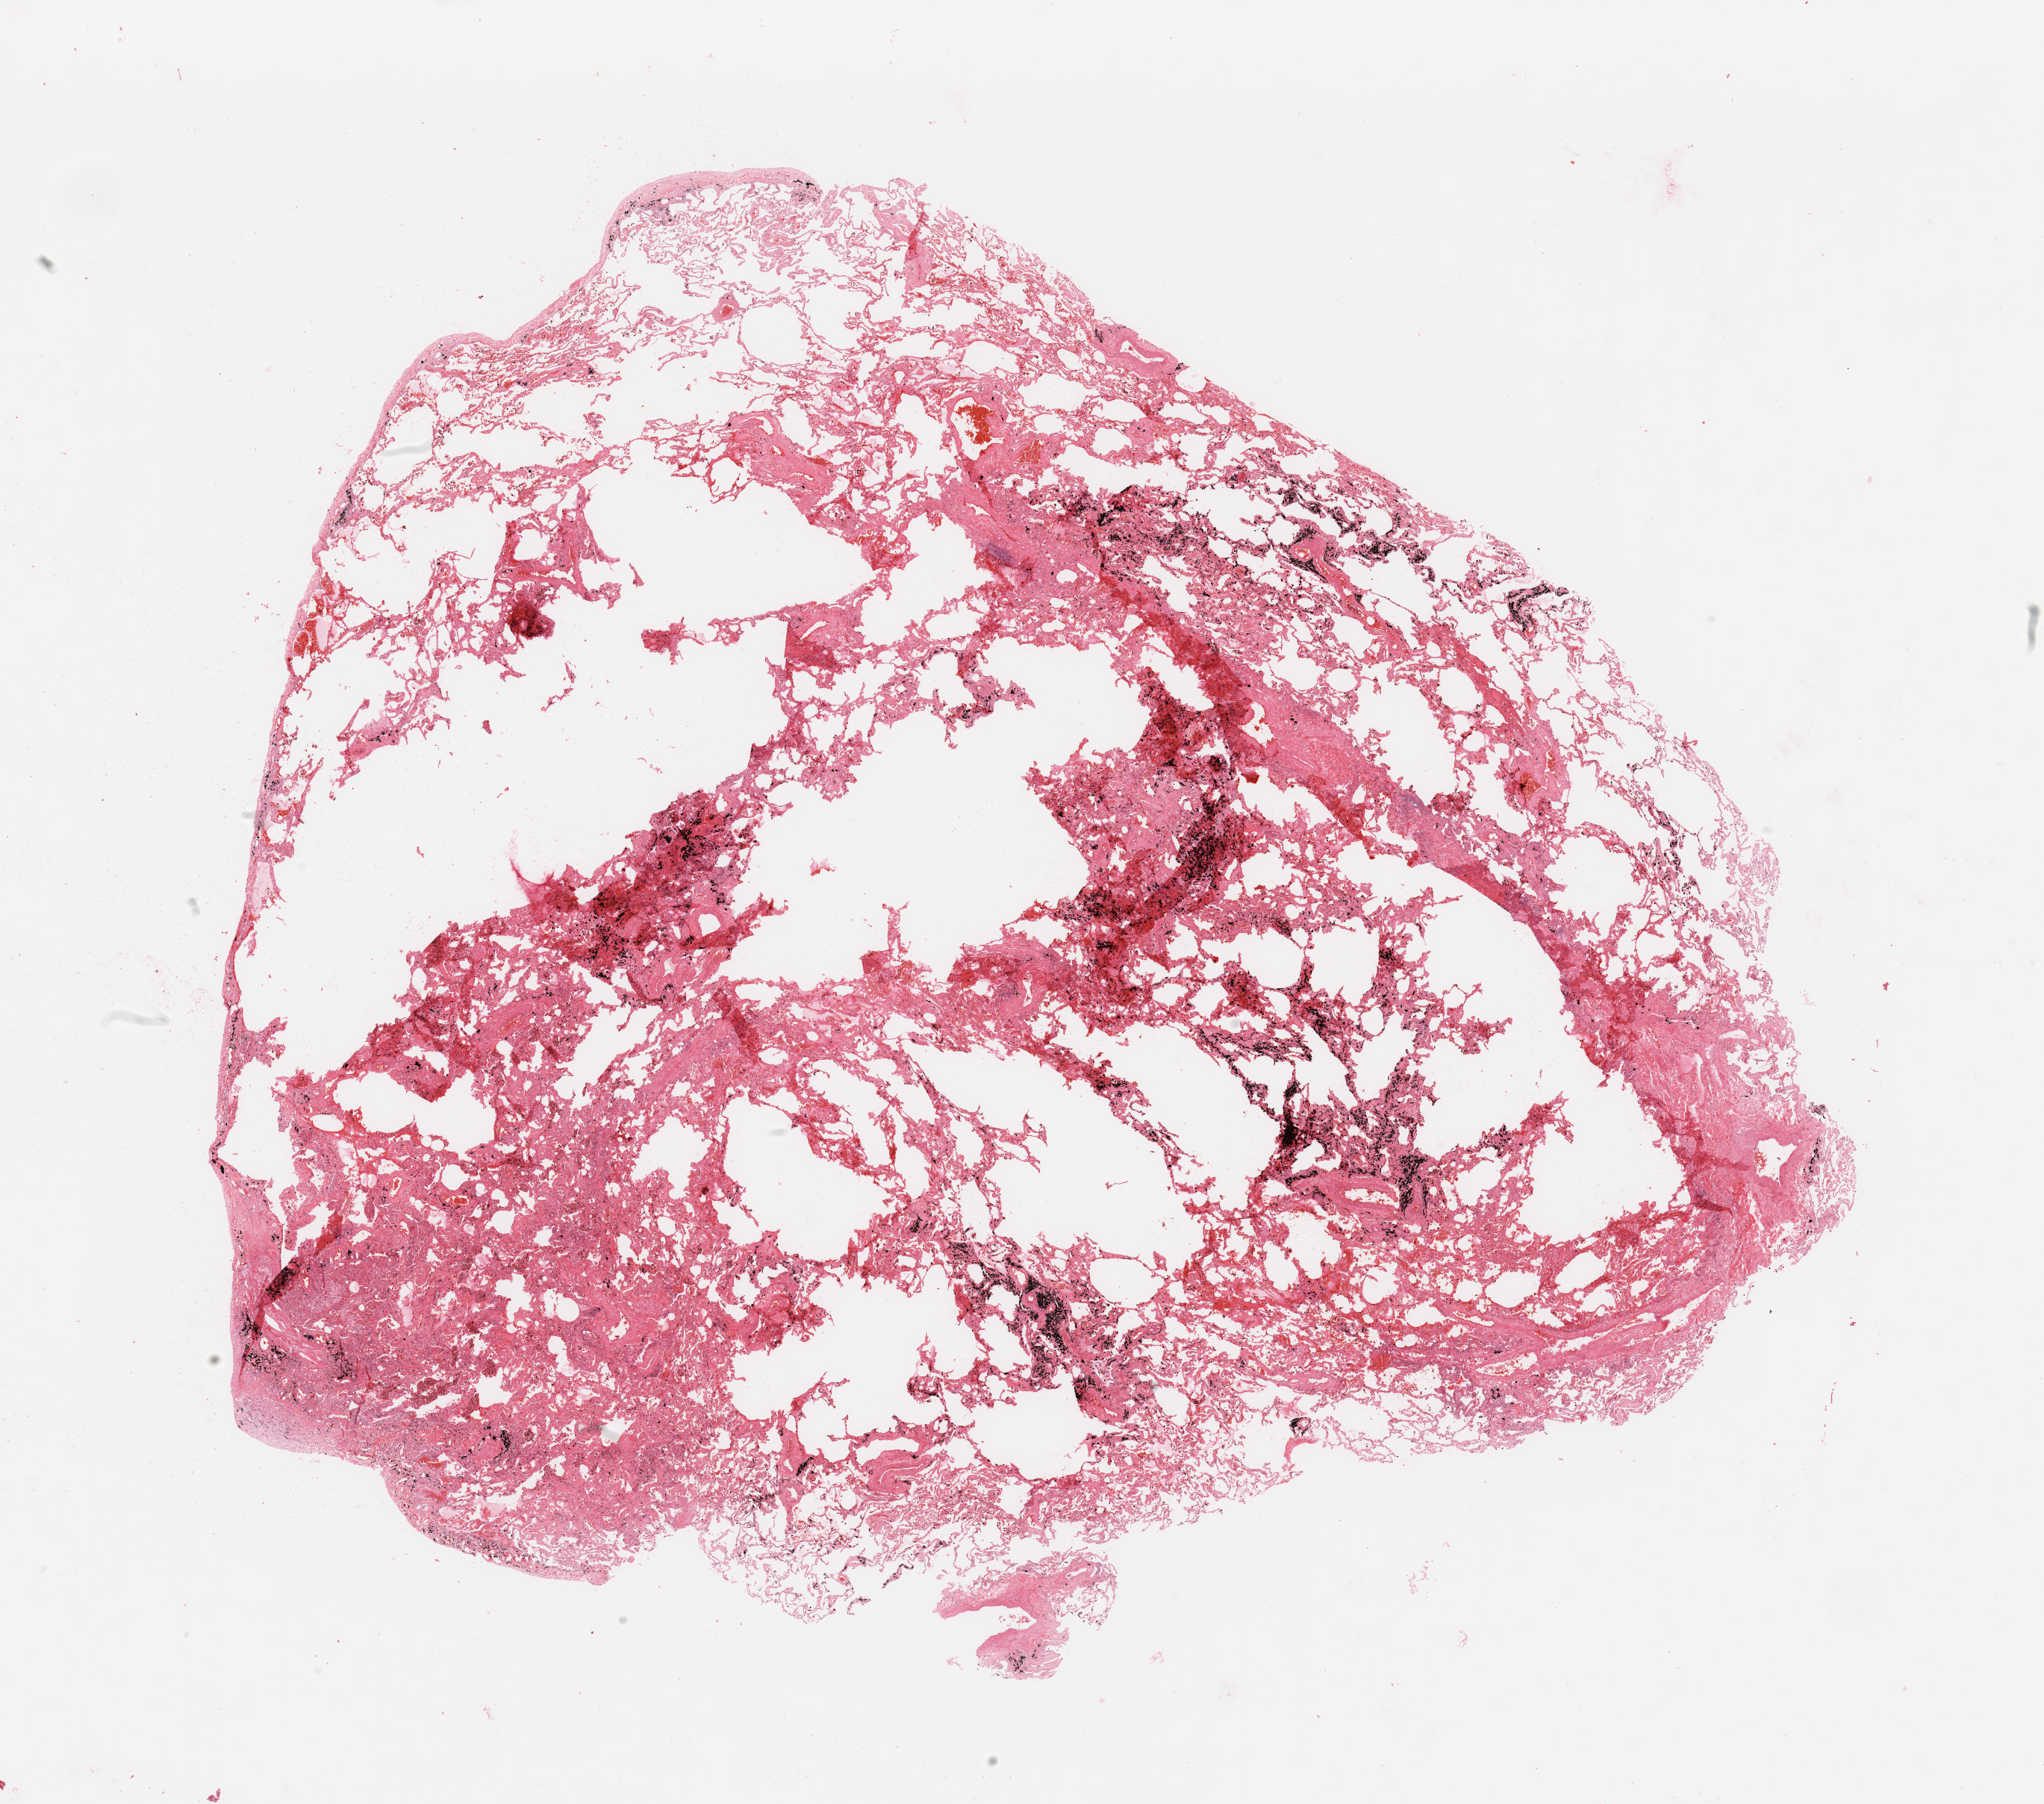
Digitized H&E tissue section (whole slide), shown as a low-resolution overview of the whole scanned area (about 21.7 x 19.1 mm). Lung, normal (non-tumour) tissue. 64-year-old male patient.
This section: normal (non-tumour) tissue from the same patient. Patient diagnosis: Adenocarcinoma, NOS.